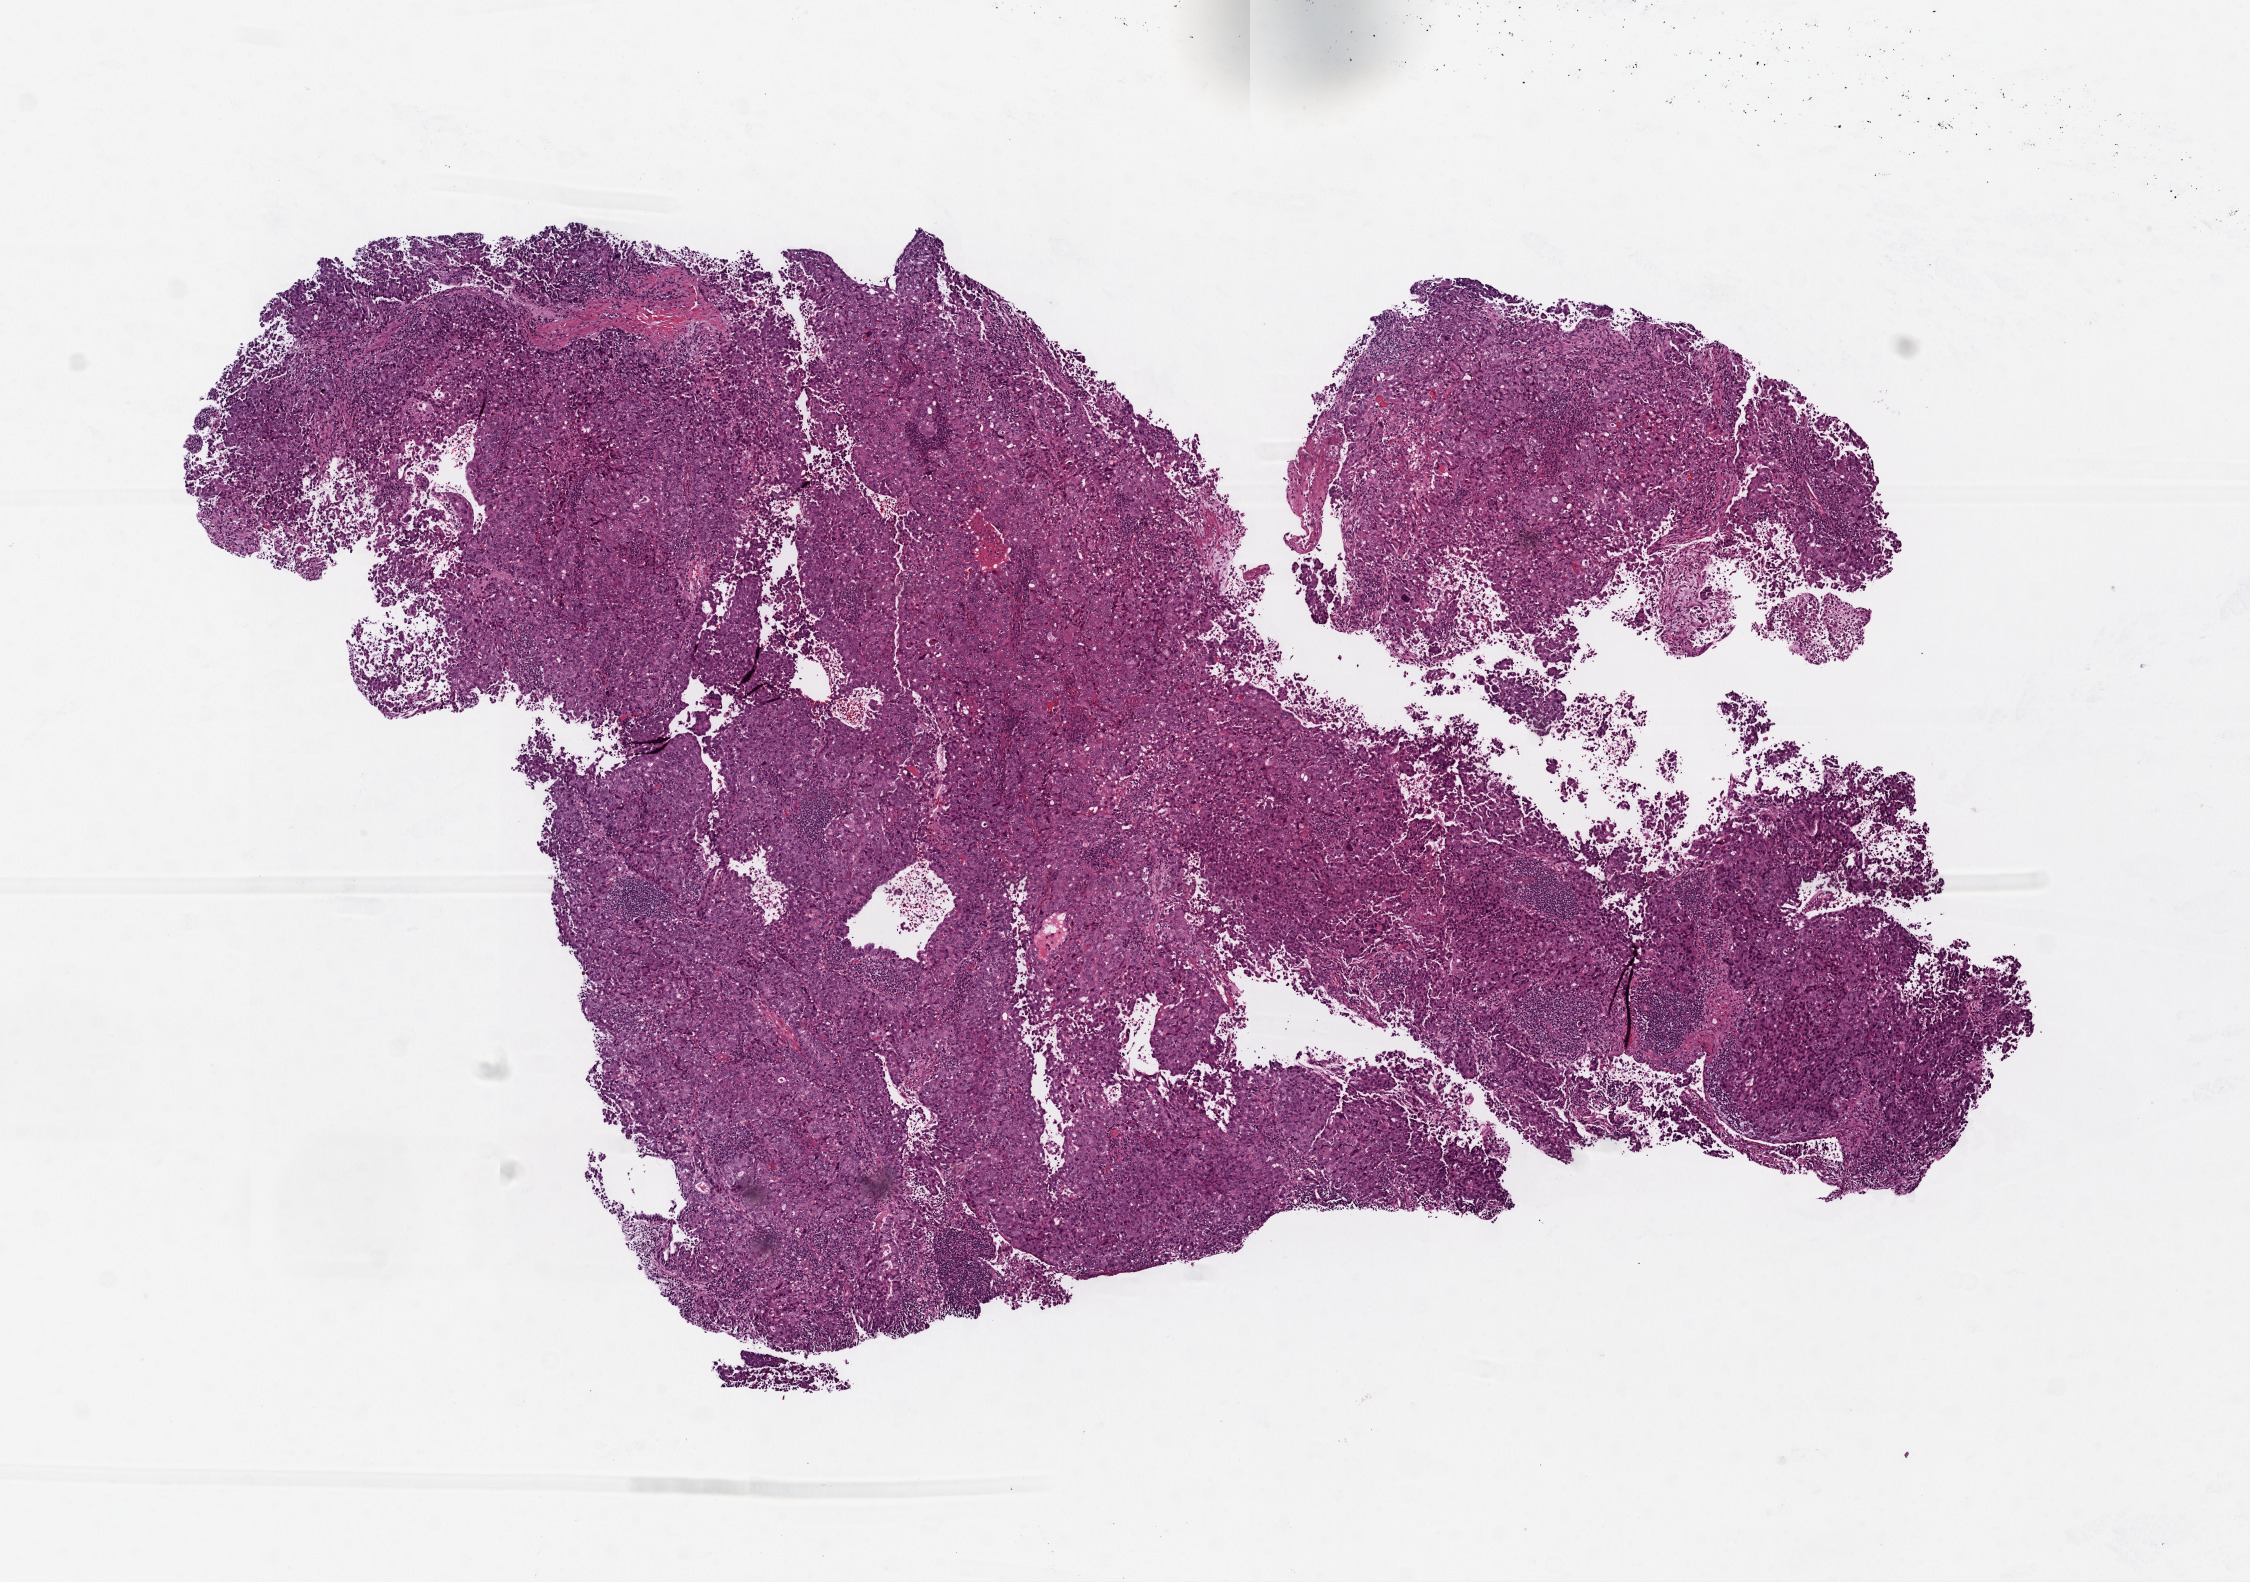
Hematoxylin and eosin (H&E) stained whole-slide image — a low-resolution overview of the entire scanned area, about 9.0 x 6.3 mm (slide scanned at 20x); frozen section from the top of the tissue portion; lung, primary tumour sample. Patient: female, age at initial diagnosis 33 years. Pathologist review of this section (percent, as recorded): tumour cells 98%, tumour nuclei 80%, stromal cells 1%, necrosis 1%. Infiltration values recorded for this section: lymphocyte infiltration 18%.
* histologic diagnosis: Adenocarcinoma, NOS (upper lobe, lung)
* laterality: right
* AJCC pathologic stage: IB (6th edition)